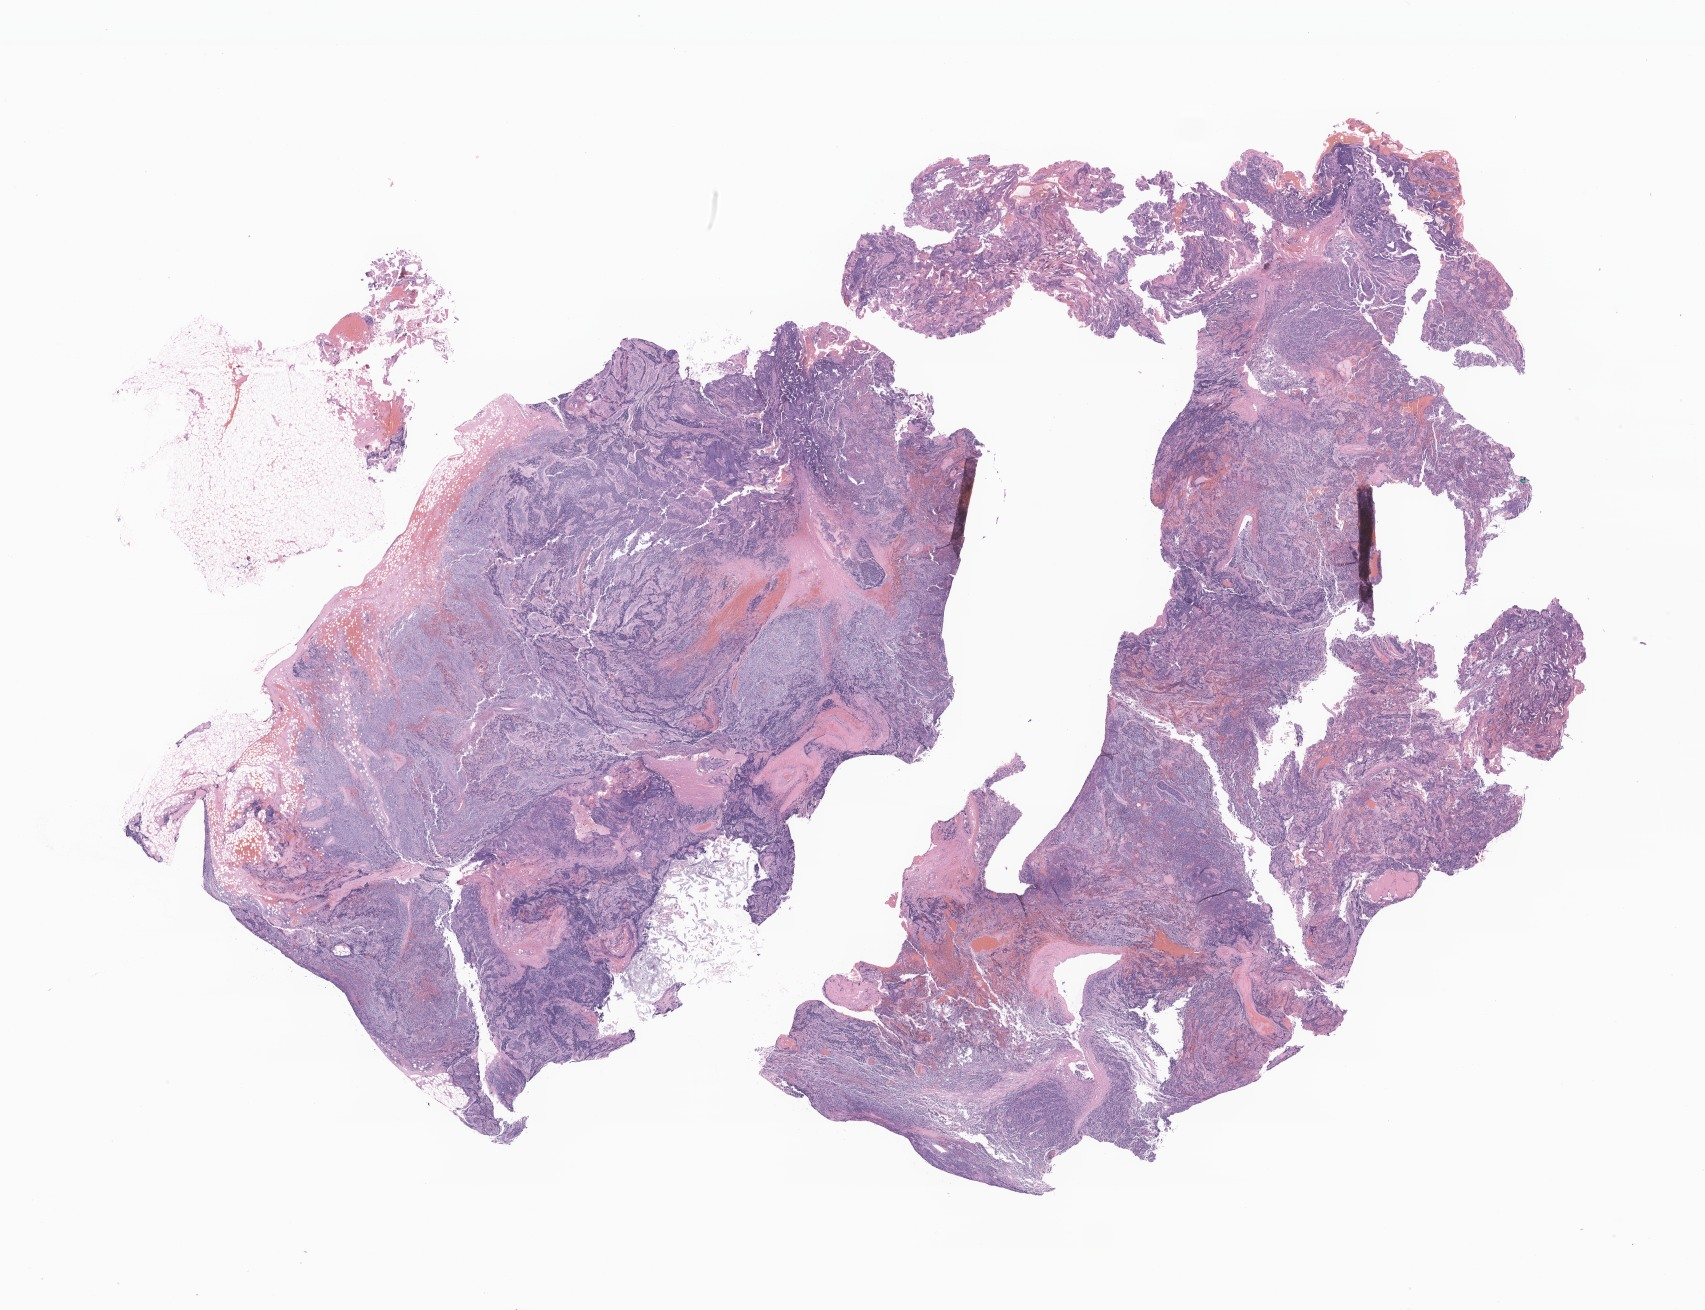
H&E whole-slide image of tumor tissue from the posterior mediastinum — whole scanned area (about 28.8 x 22.1 mm) shown as a low-resolution overview. Formalin-fixed, paraffin-embedded (FFPE) tissue. Male patient, age 105 months (8 years 9 months).
Diagnosis (ICD-O-3 morphology term): Neuroblastoma, NOS.